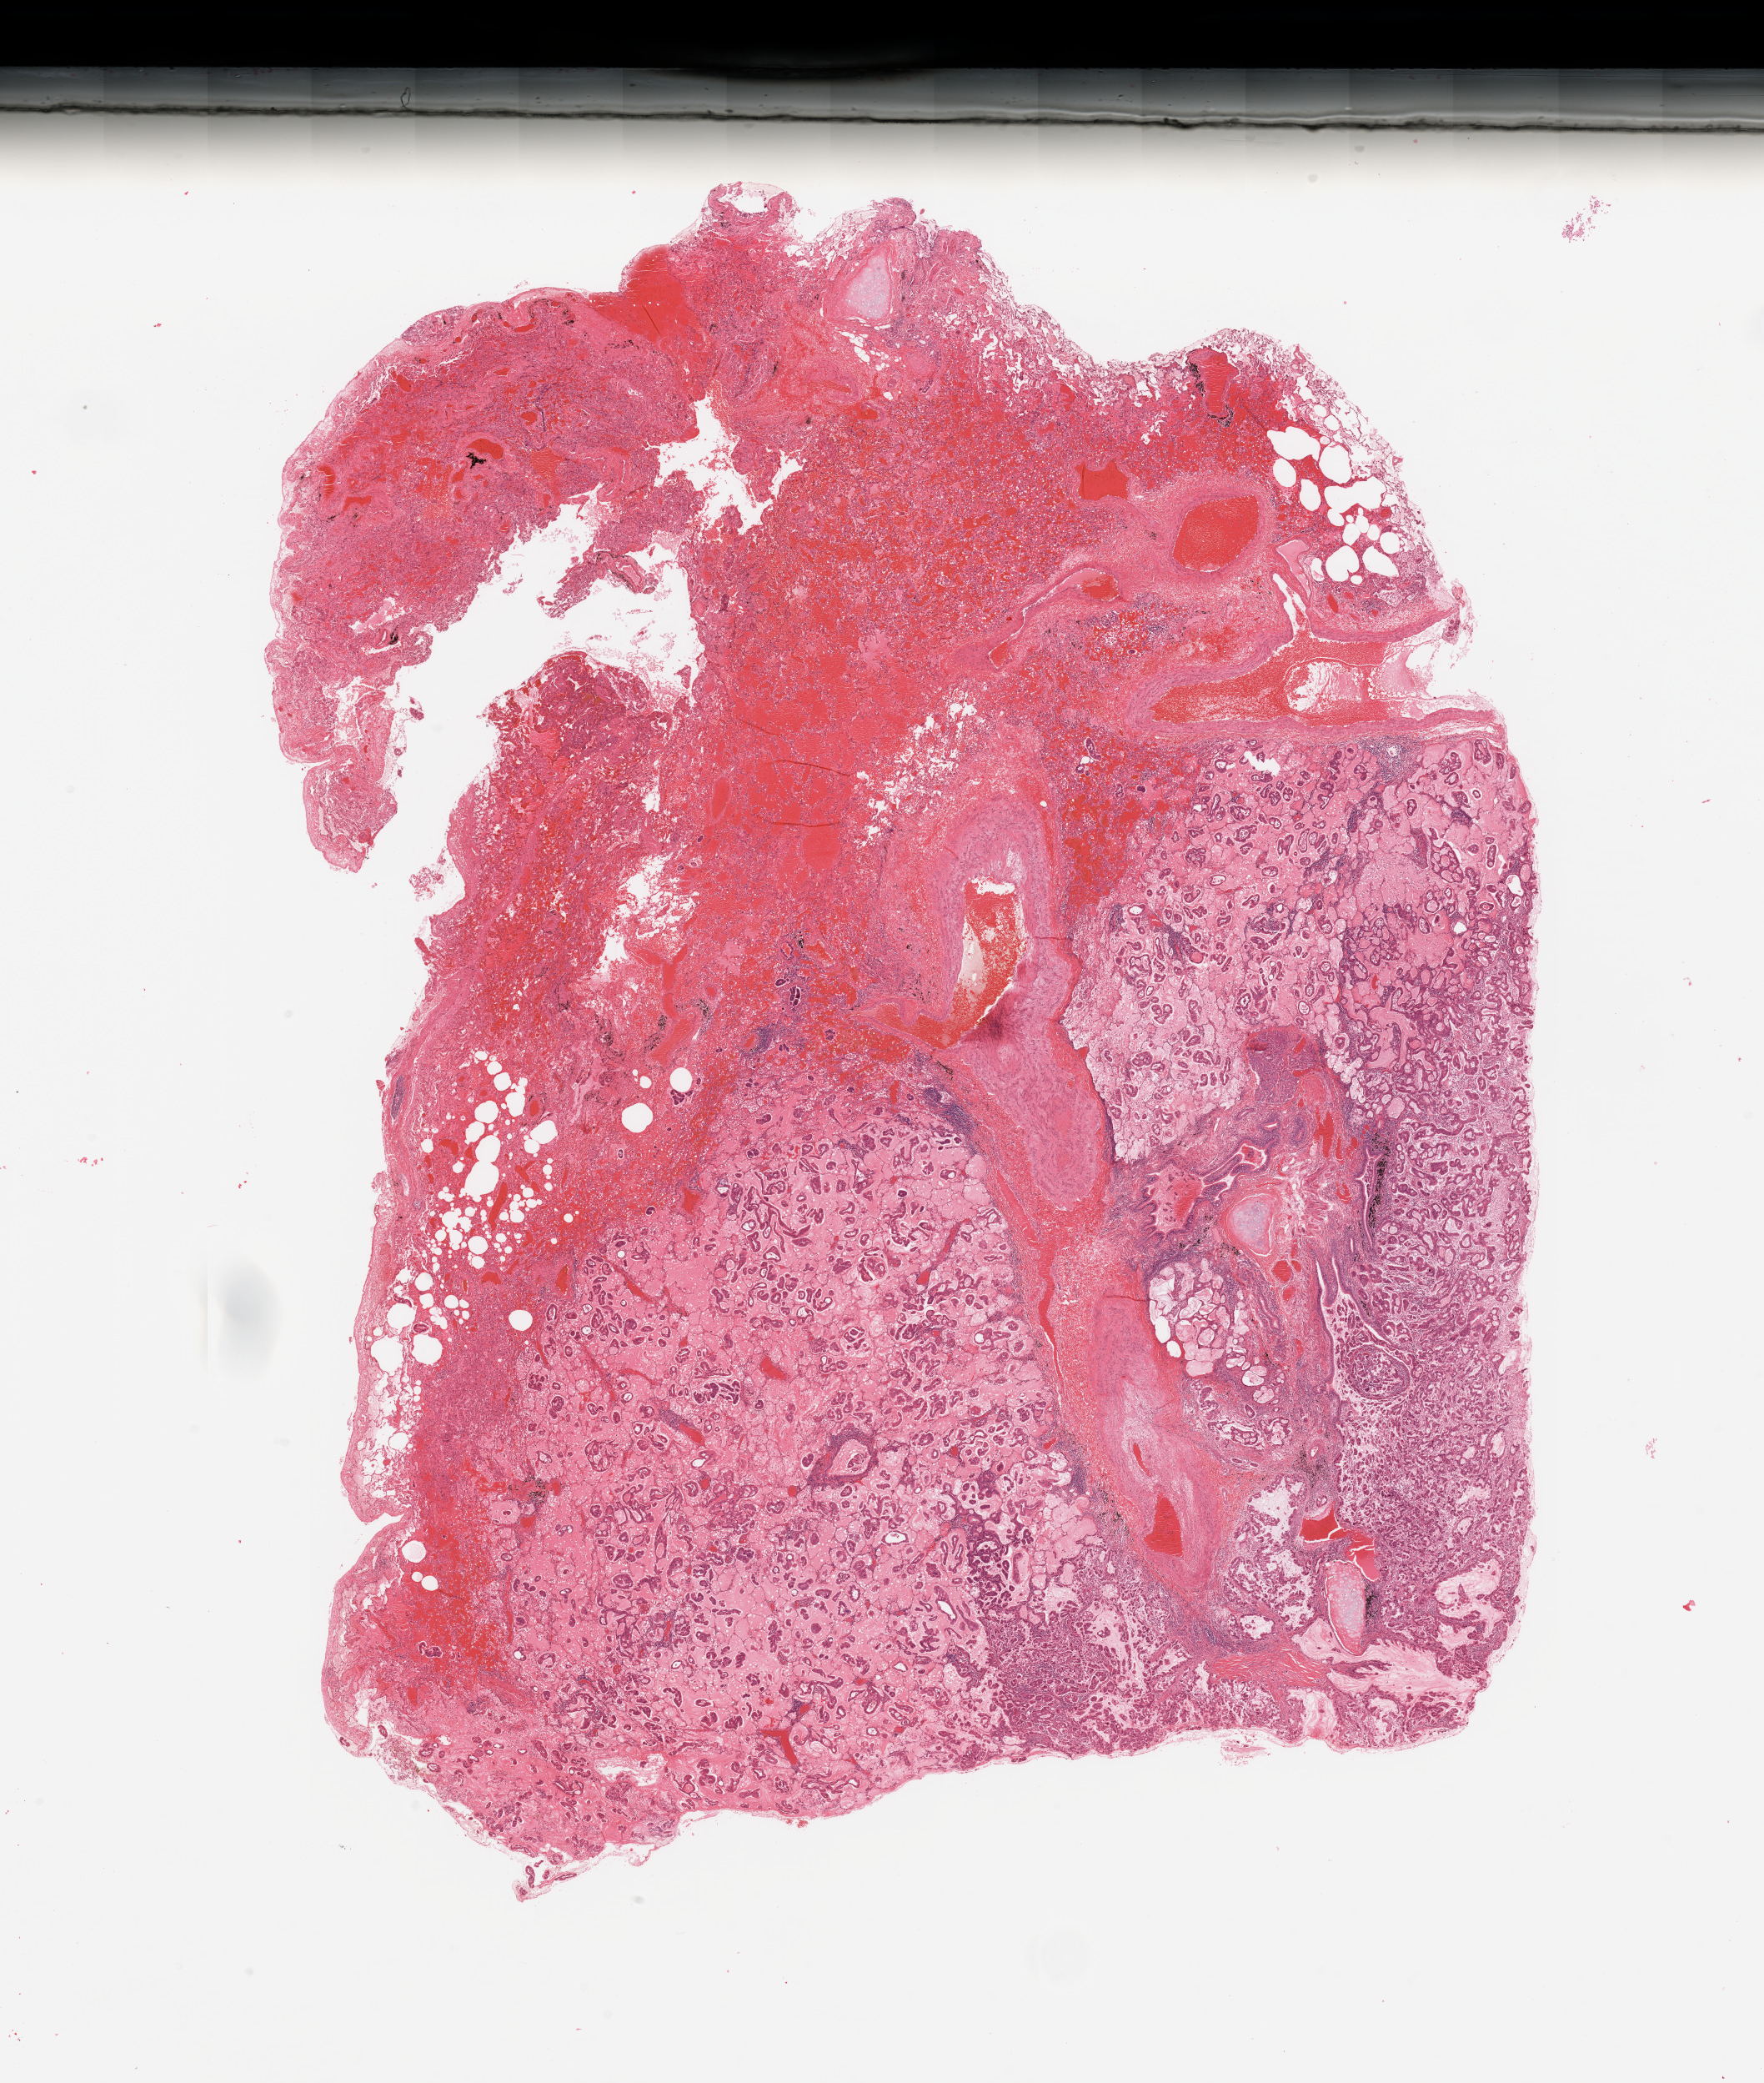
Whole-slide histology image, H&E-stained — shown as a low-resolution overview of the whole scanned area (about 16.7 x 19.8 mm, slide scanned at 20x), lung, tumour tissue. Female, 52 y/o. Histologic grade: G2 (moderately differentiated).
- AJCC pathologic stage: IIA
- primary tumour site (as recorded): left lower lobe
- histologic diagnosis: Adenocarcinoma, NOS